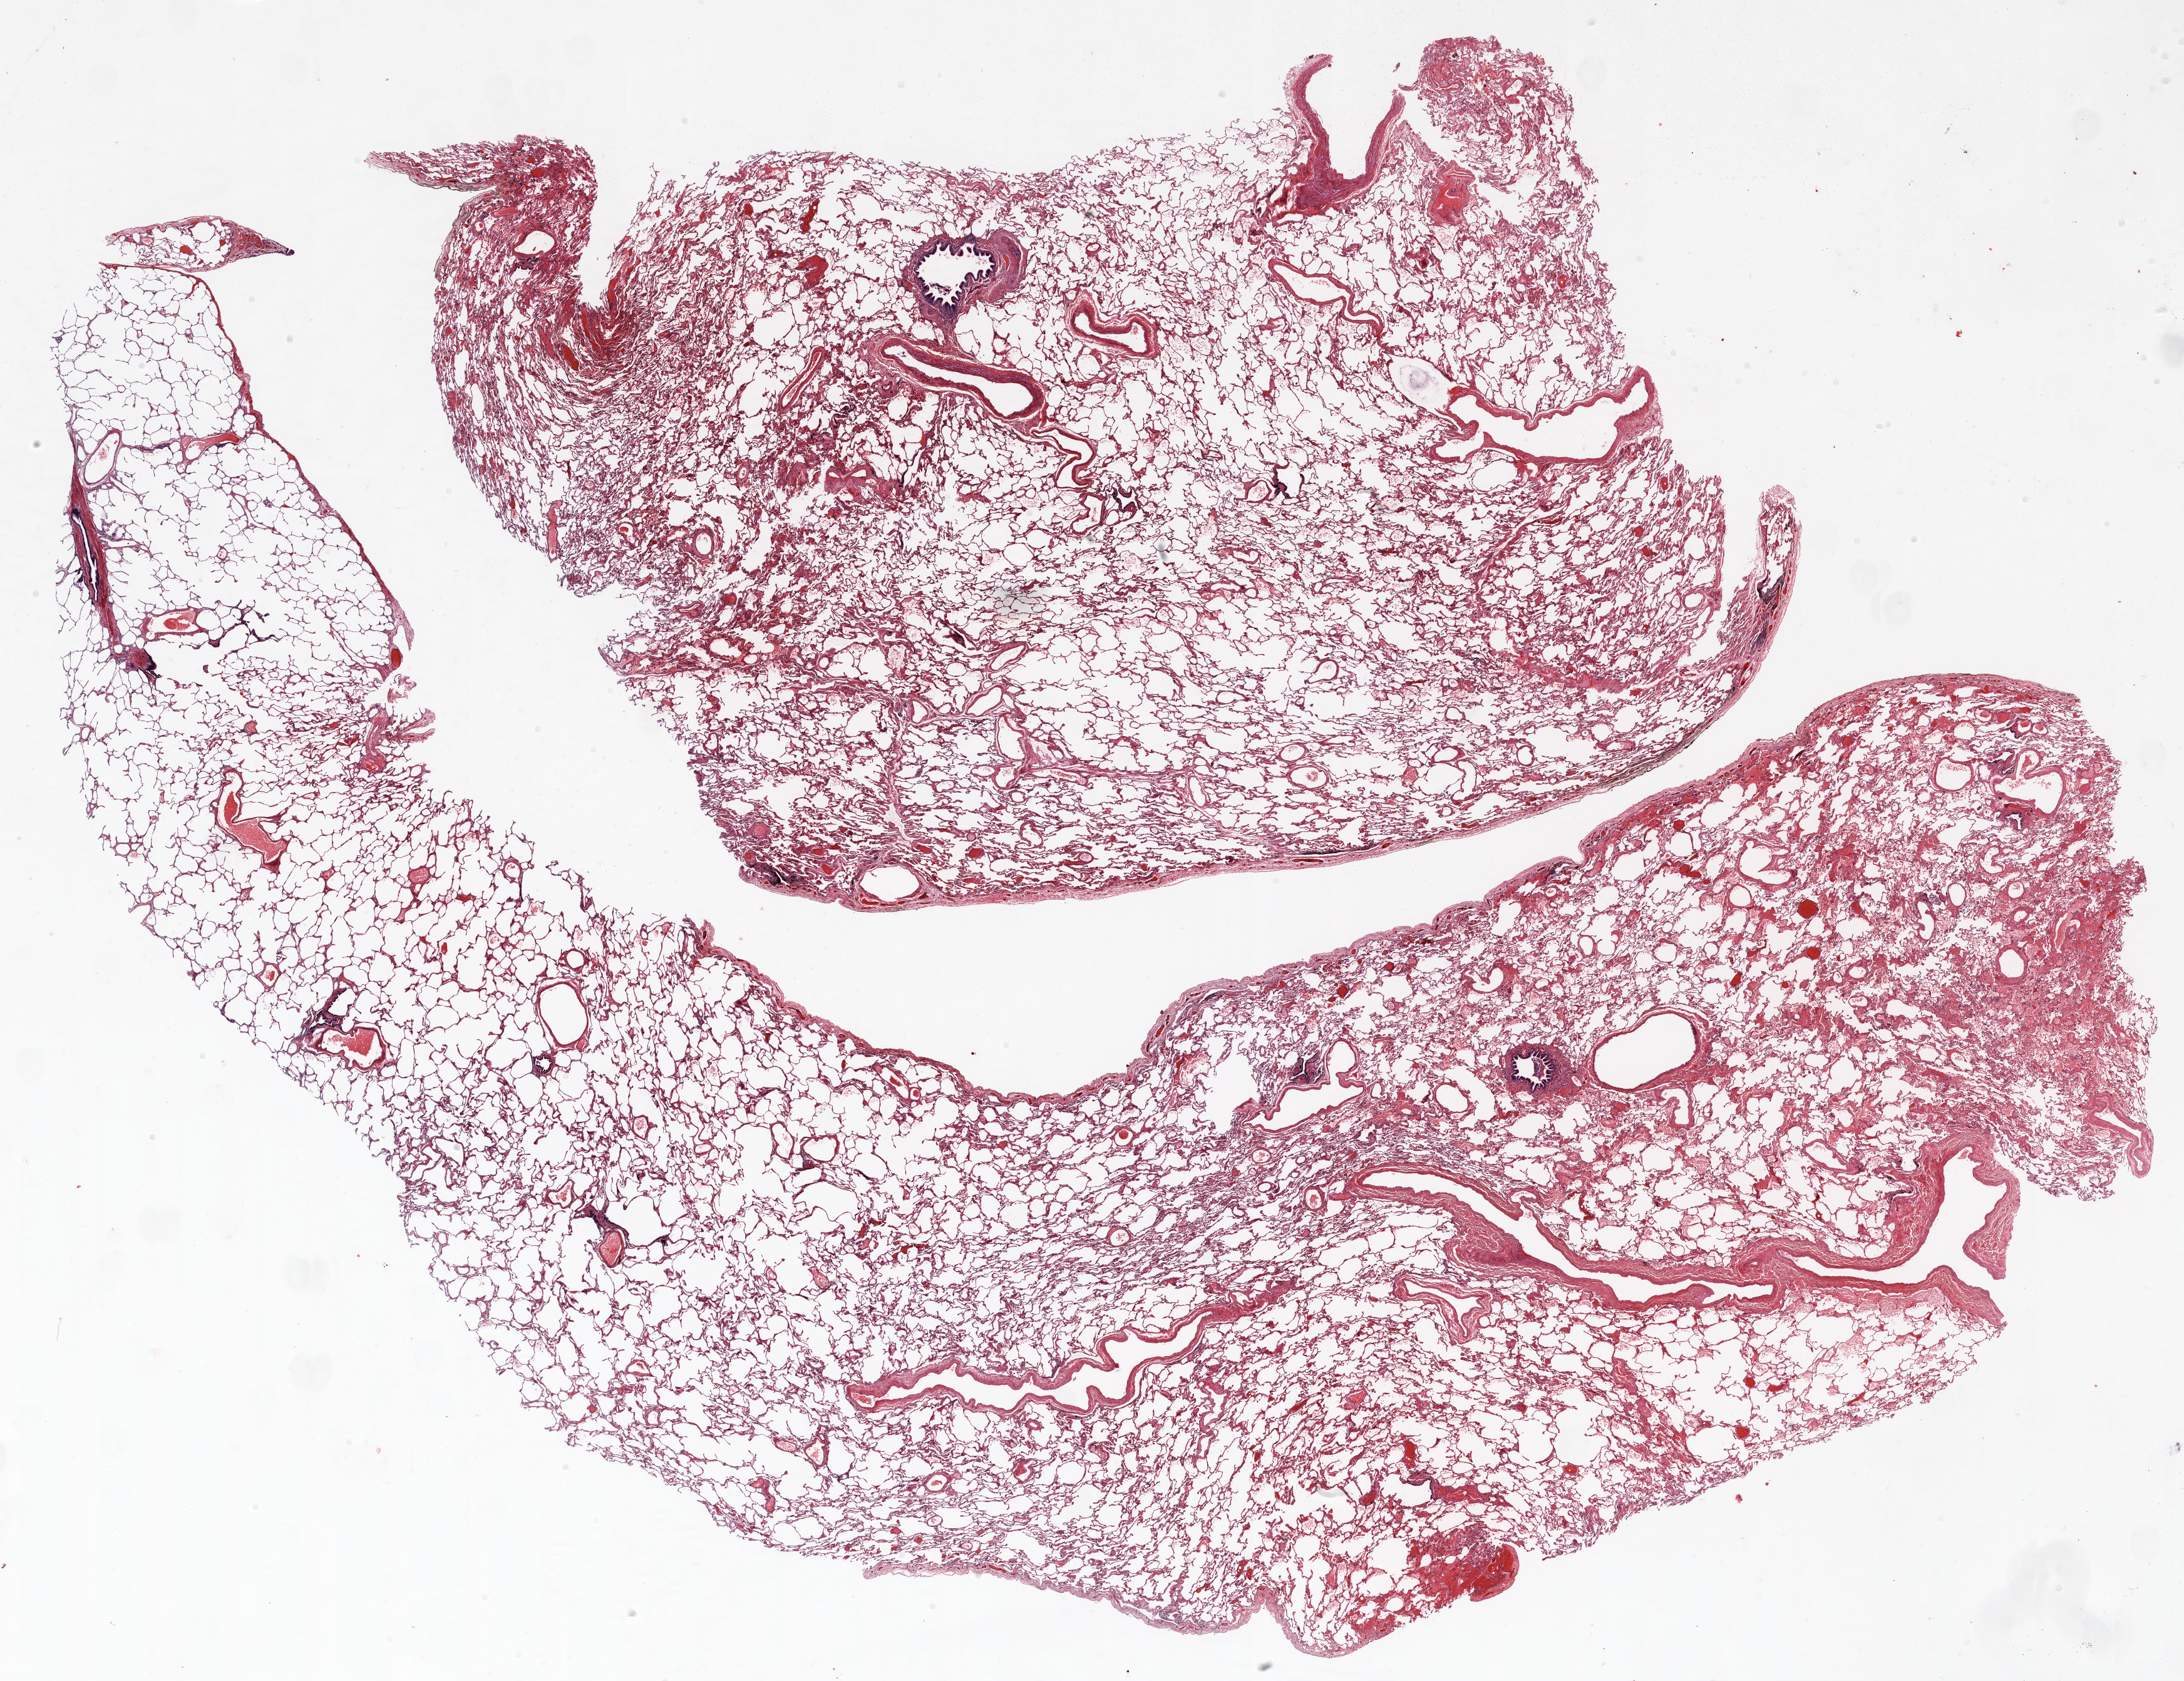
H&E whole-slide image — whole scanned area (about 28.0 x 21.6 mm) shown as a low-resolution overview. FFPE section. Lung tissue. Female patient, aged 61 at enrolment. Former smoker at enrolment. Grade: well differentiated (G1).
Primary tumour location (clinical record): left lower lobe. Tumour size (pathology): 10 mm. Stage (AJCC 6th edition): IA. Participant's lung-cancer diagnosis: Bronchiolo-alveolar adenocarcinoma, NOS (ICD-O-3 8250/3).